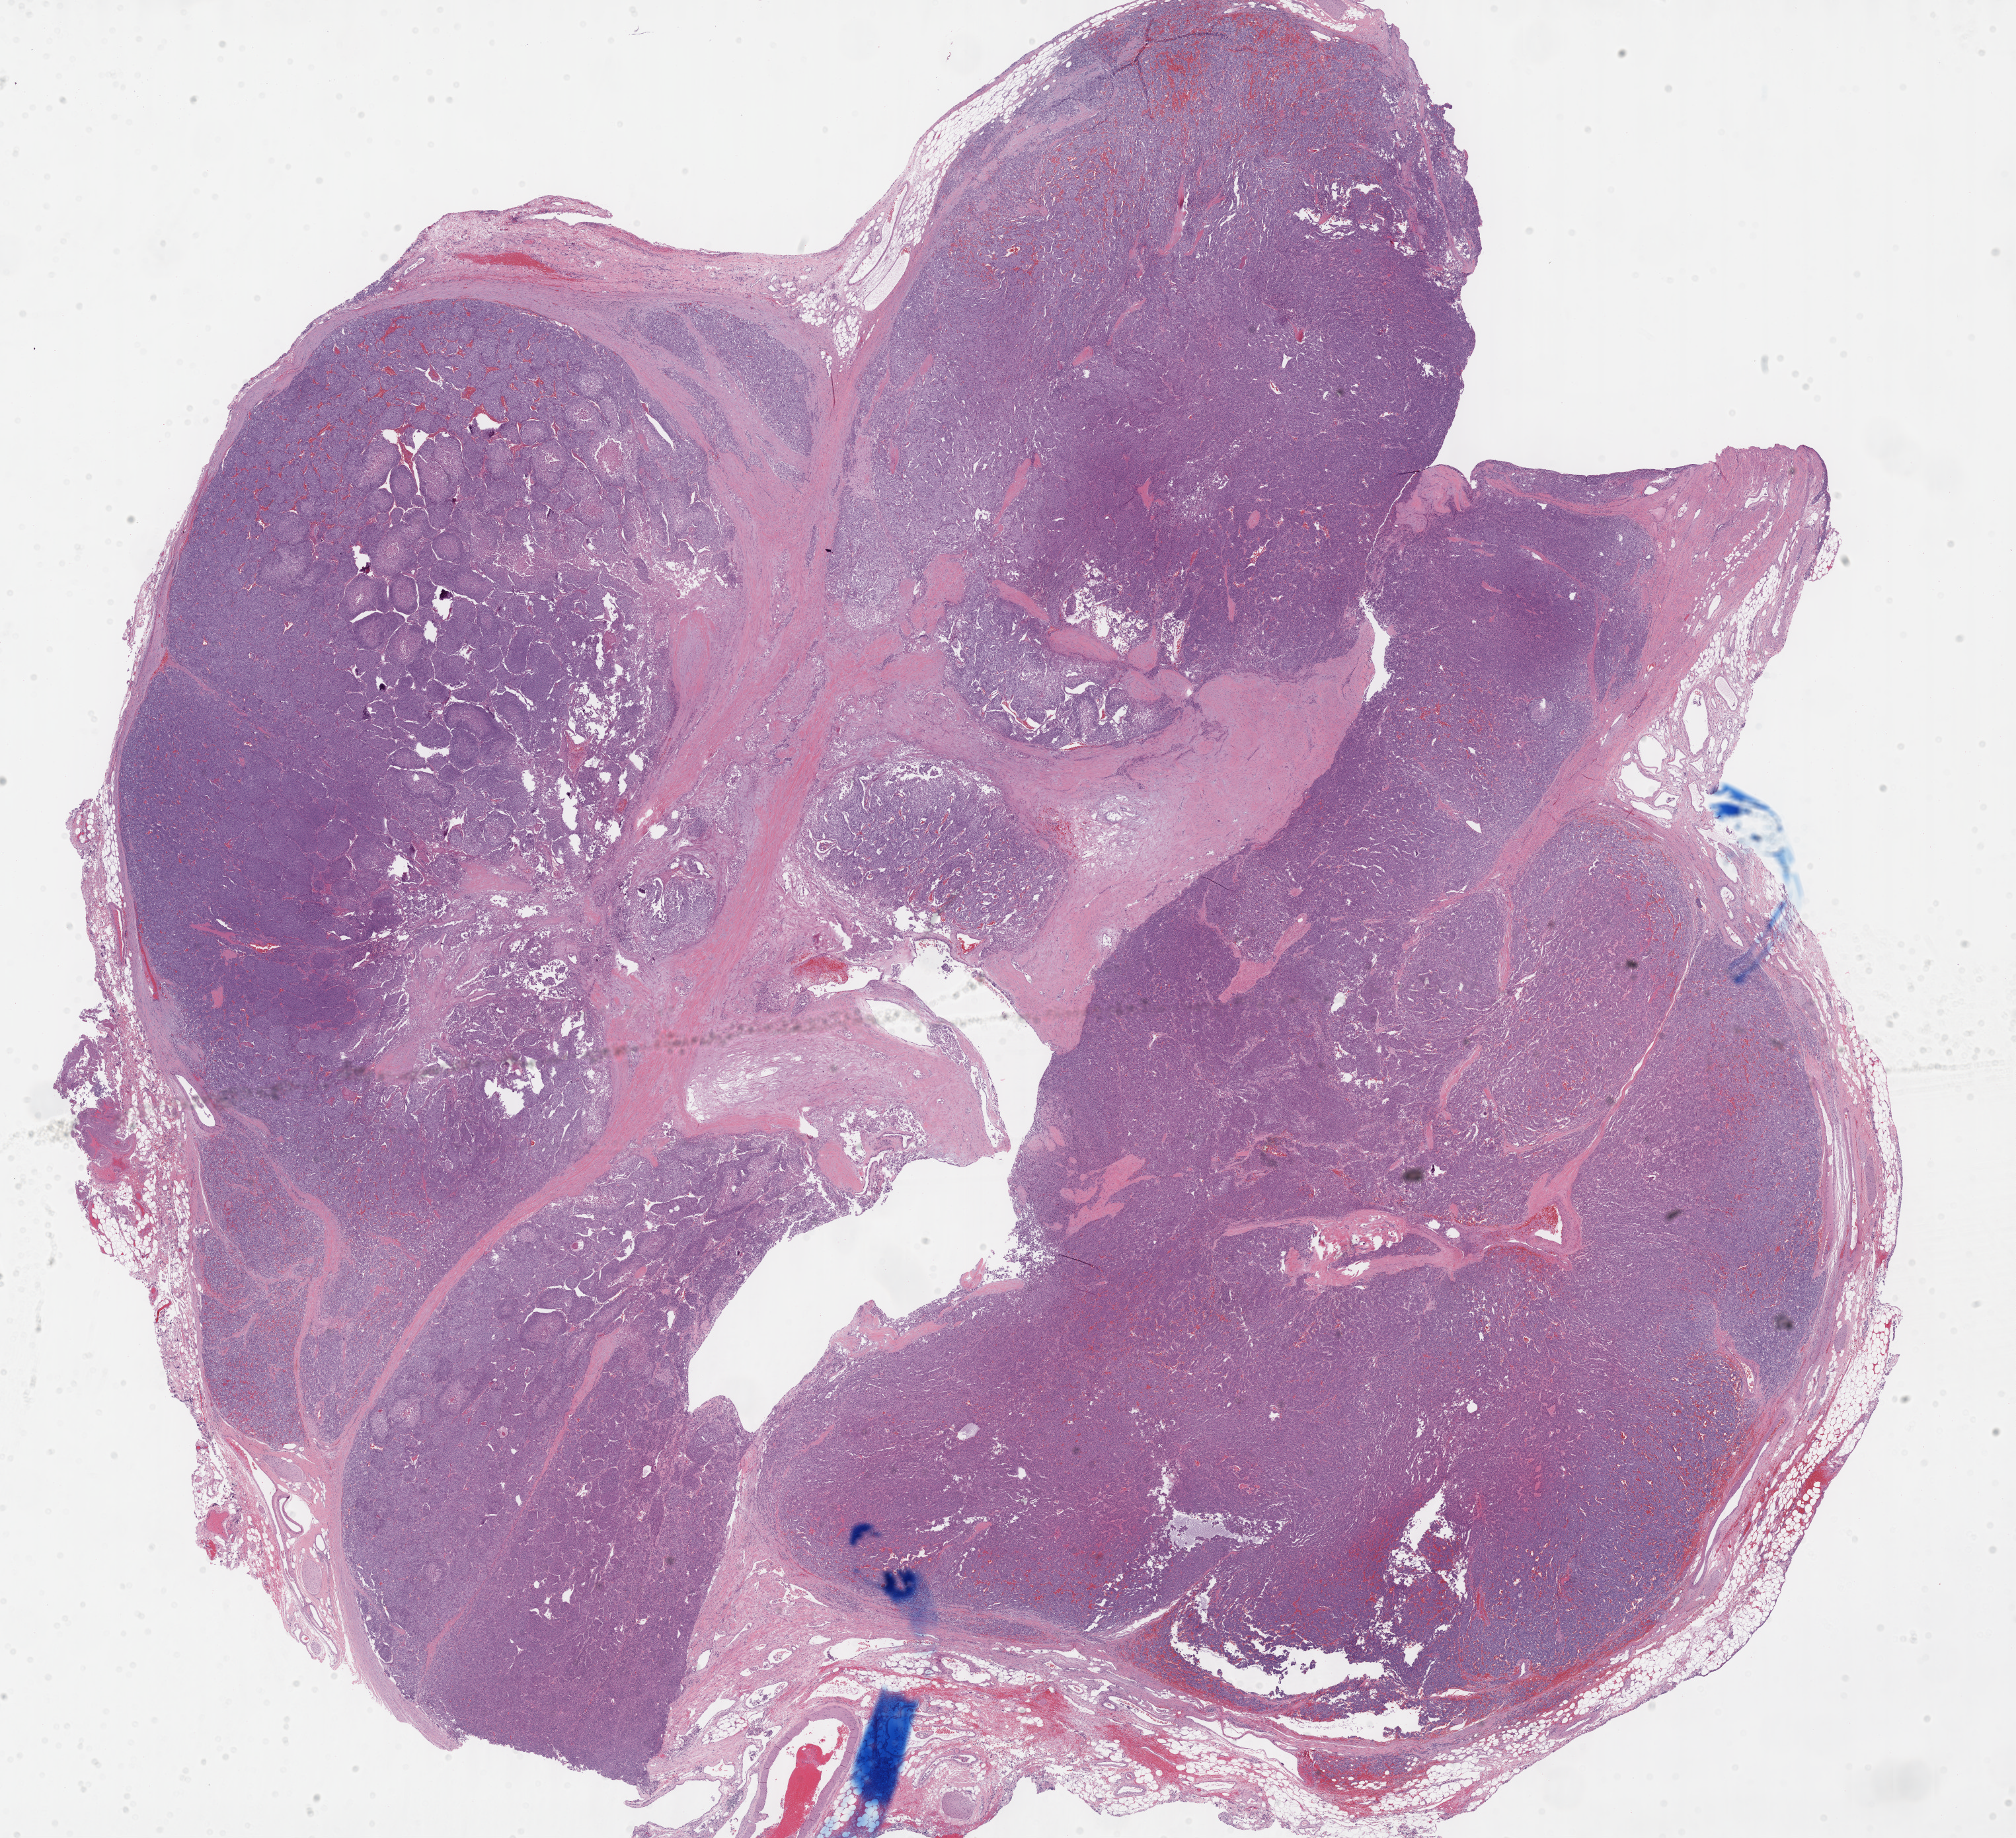
H&E whole-slide image, shown as a low-resolution overview of the whole scanned area (about 24.6 x 22.5 mm, slide scanned at 40x), FFPE section, sample: primary tumour, adrenal gland. Patient: male, age at initial diagnosis 66 years.
Lymph nodes positive (case pathology): 0 of 4 examined. Laterality: left. Histologic diagnosis: Pheochromocytoma, malignant.